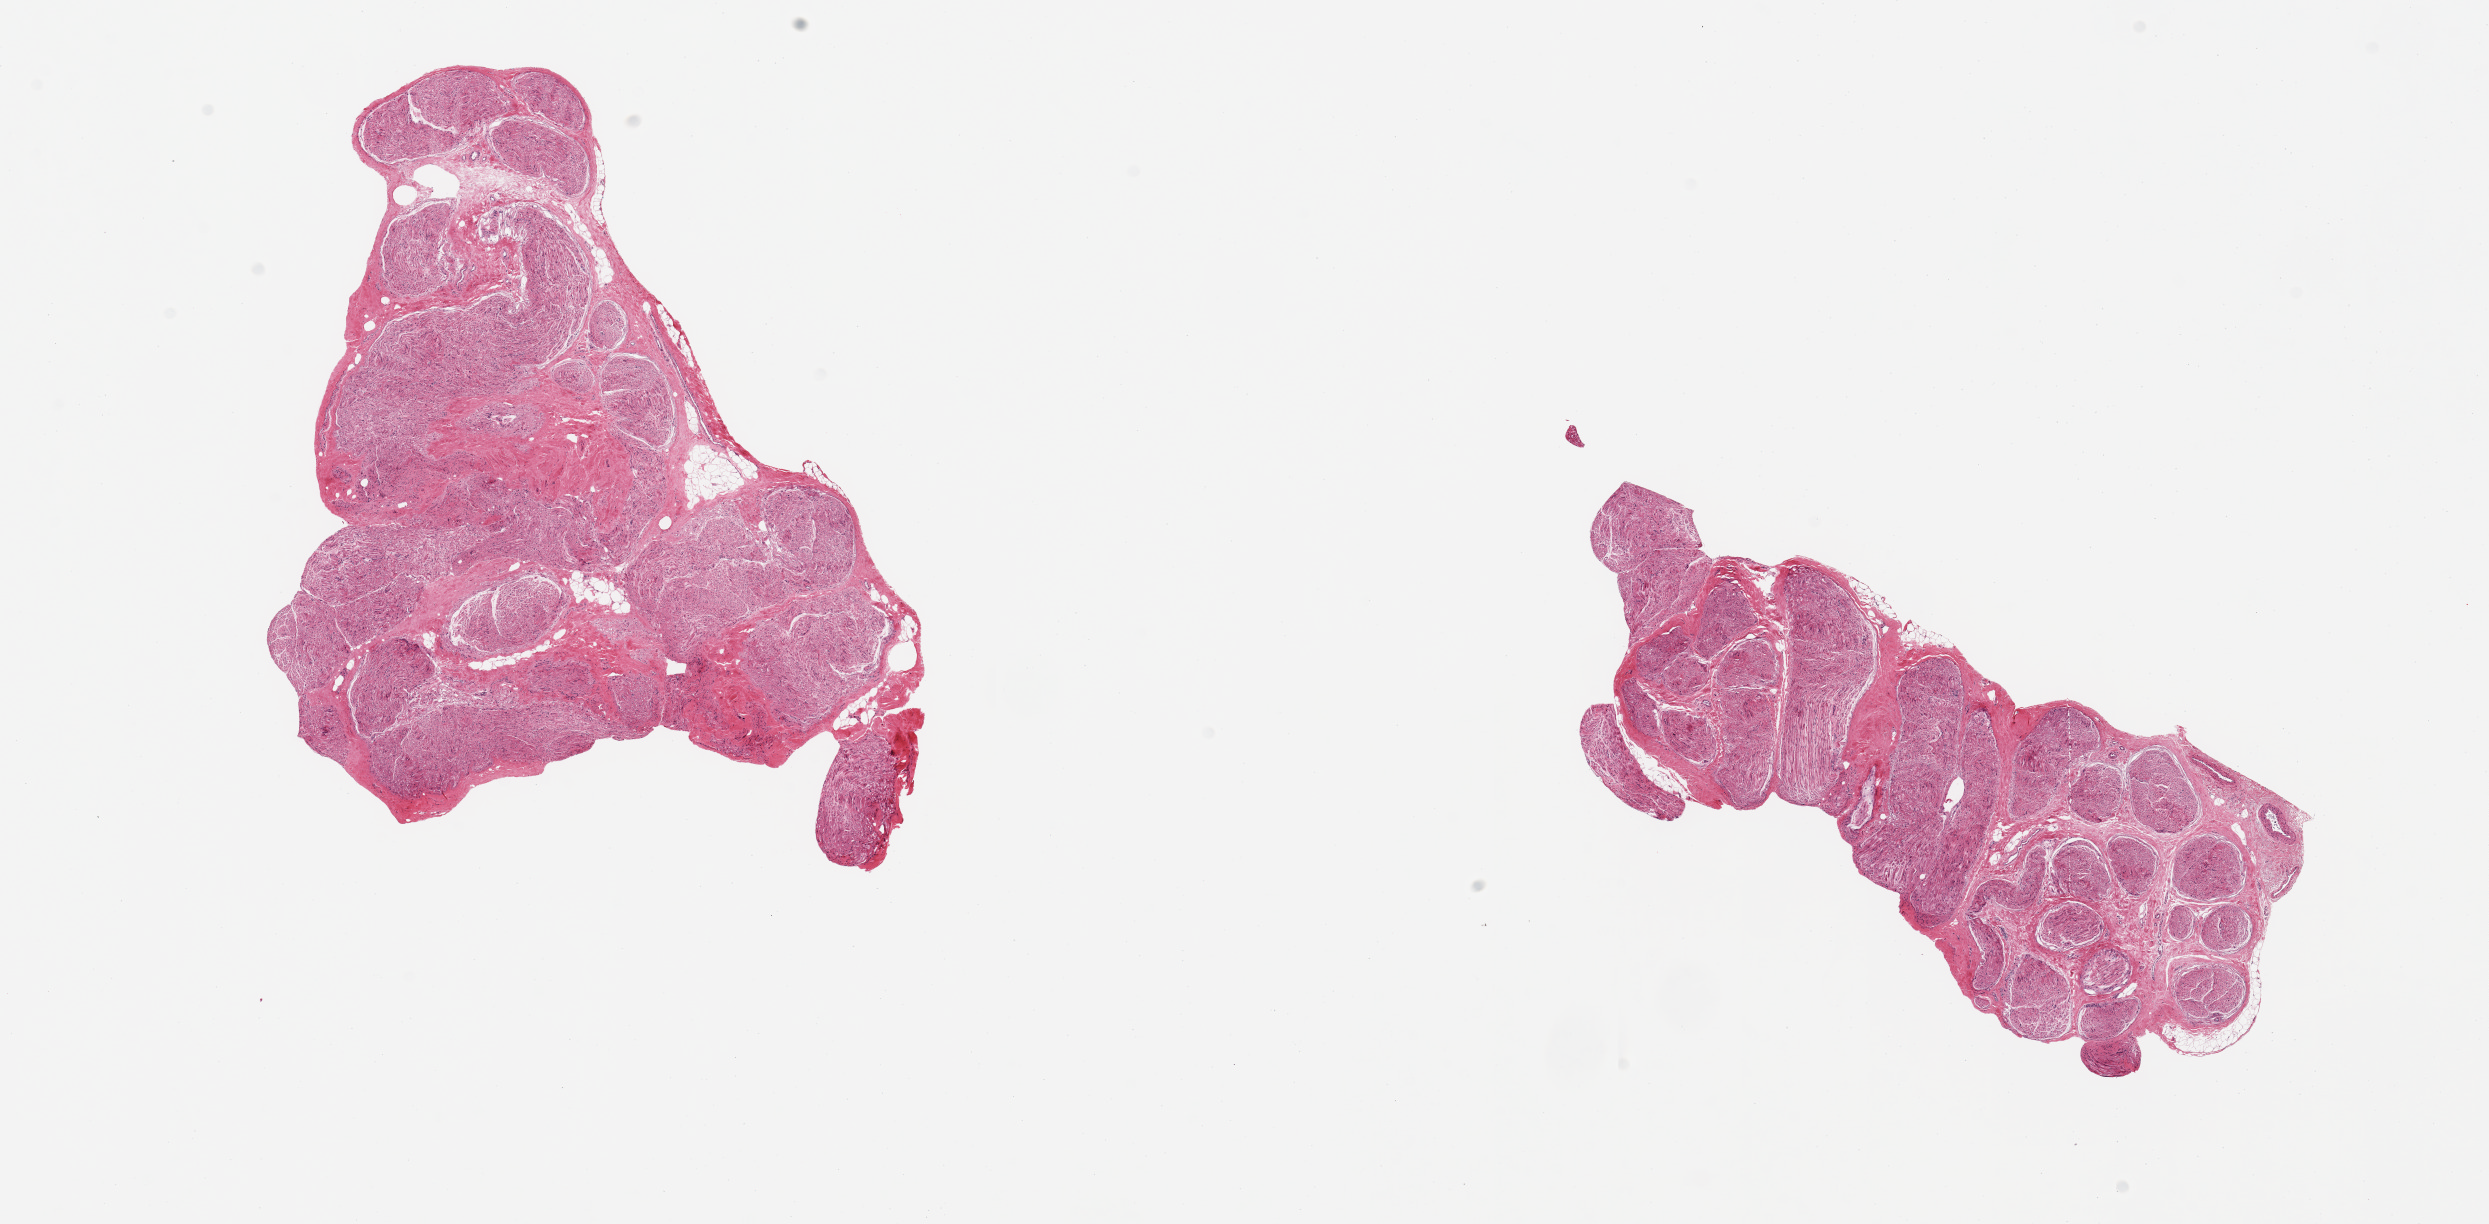
Whole-slide image, hematoxylin and eosin (H&E) stain, whole scanned area (about 19.7 x 9.7 mm, from a 20x scan) shown as a low-resolution overview; PAXgene-fixed paraffin-embedded (PFPE) section; section of tibial nerve (target tissue); donor tissue sample. Male donor.
* reviewer comment on this tissue sample: 2 pieces; <5% fat